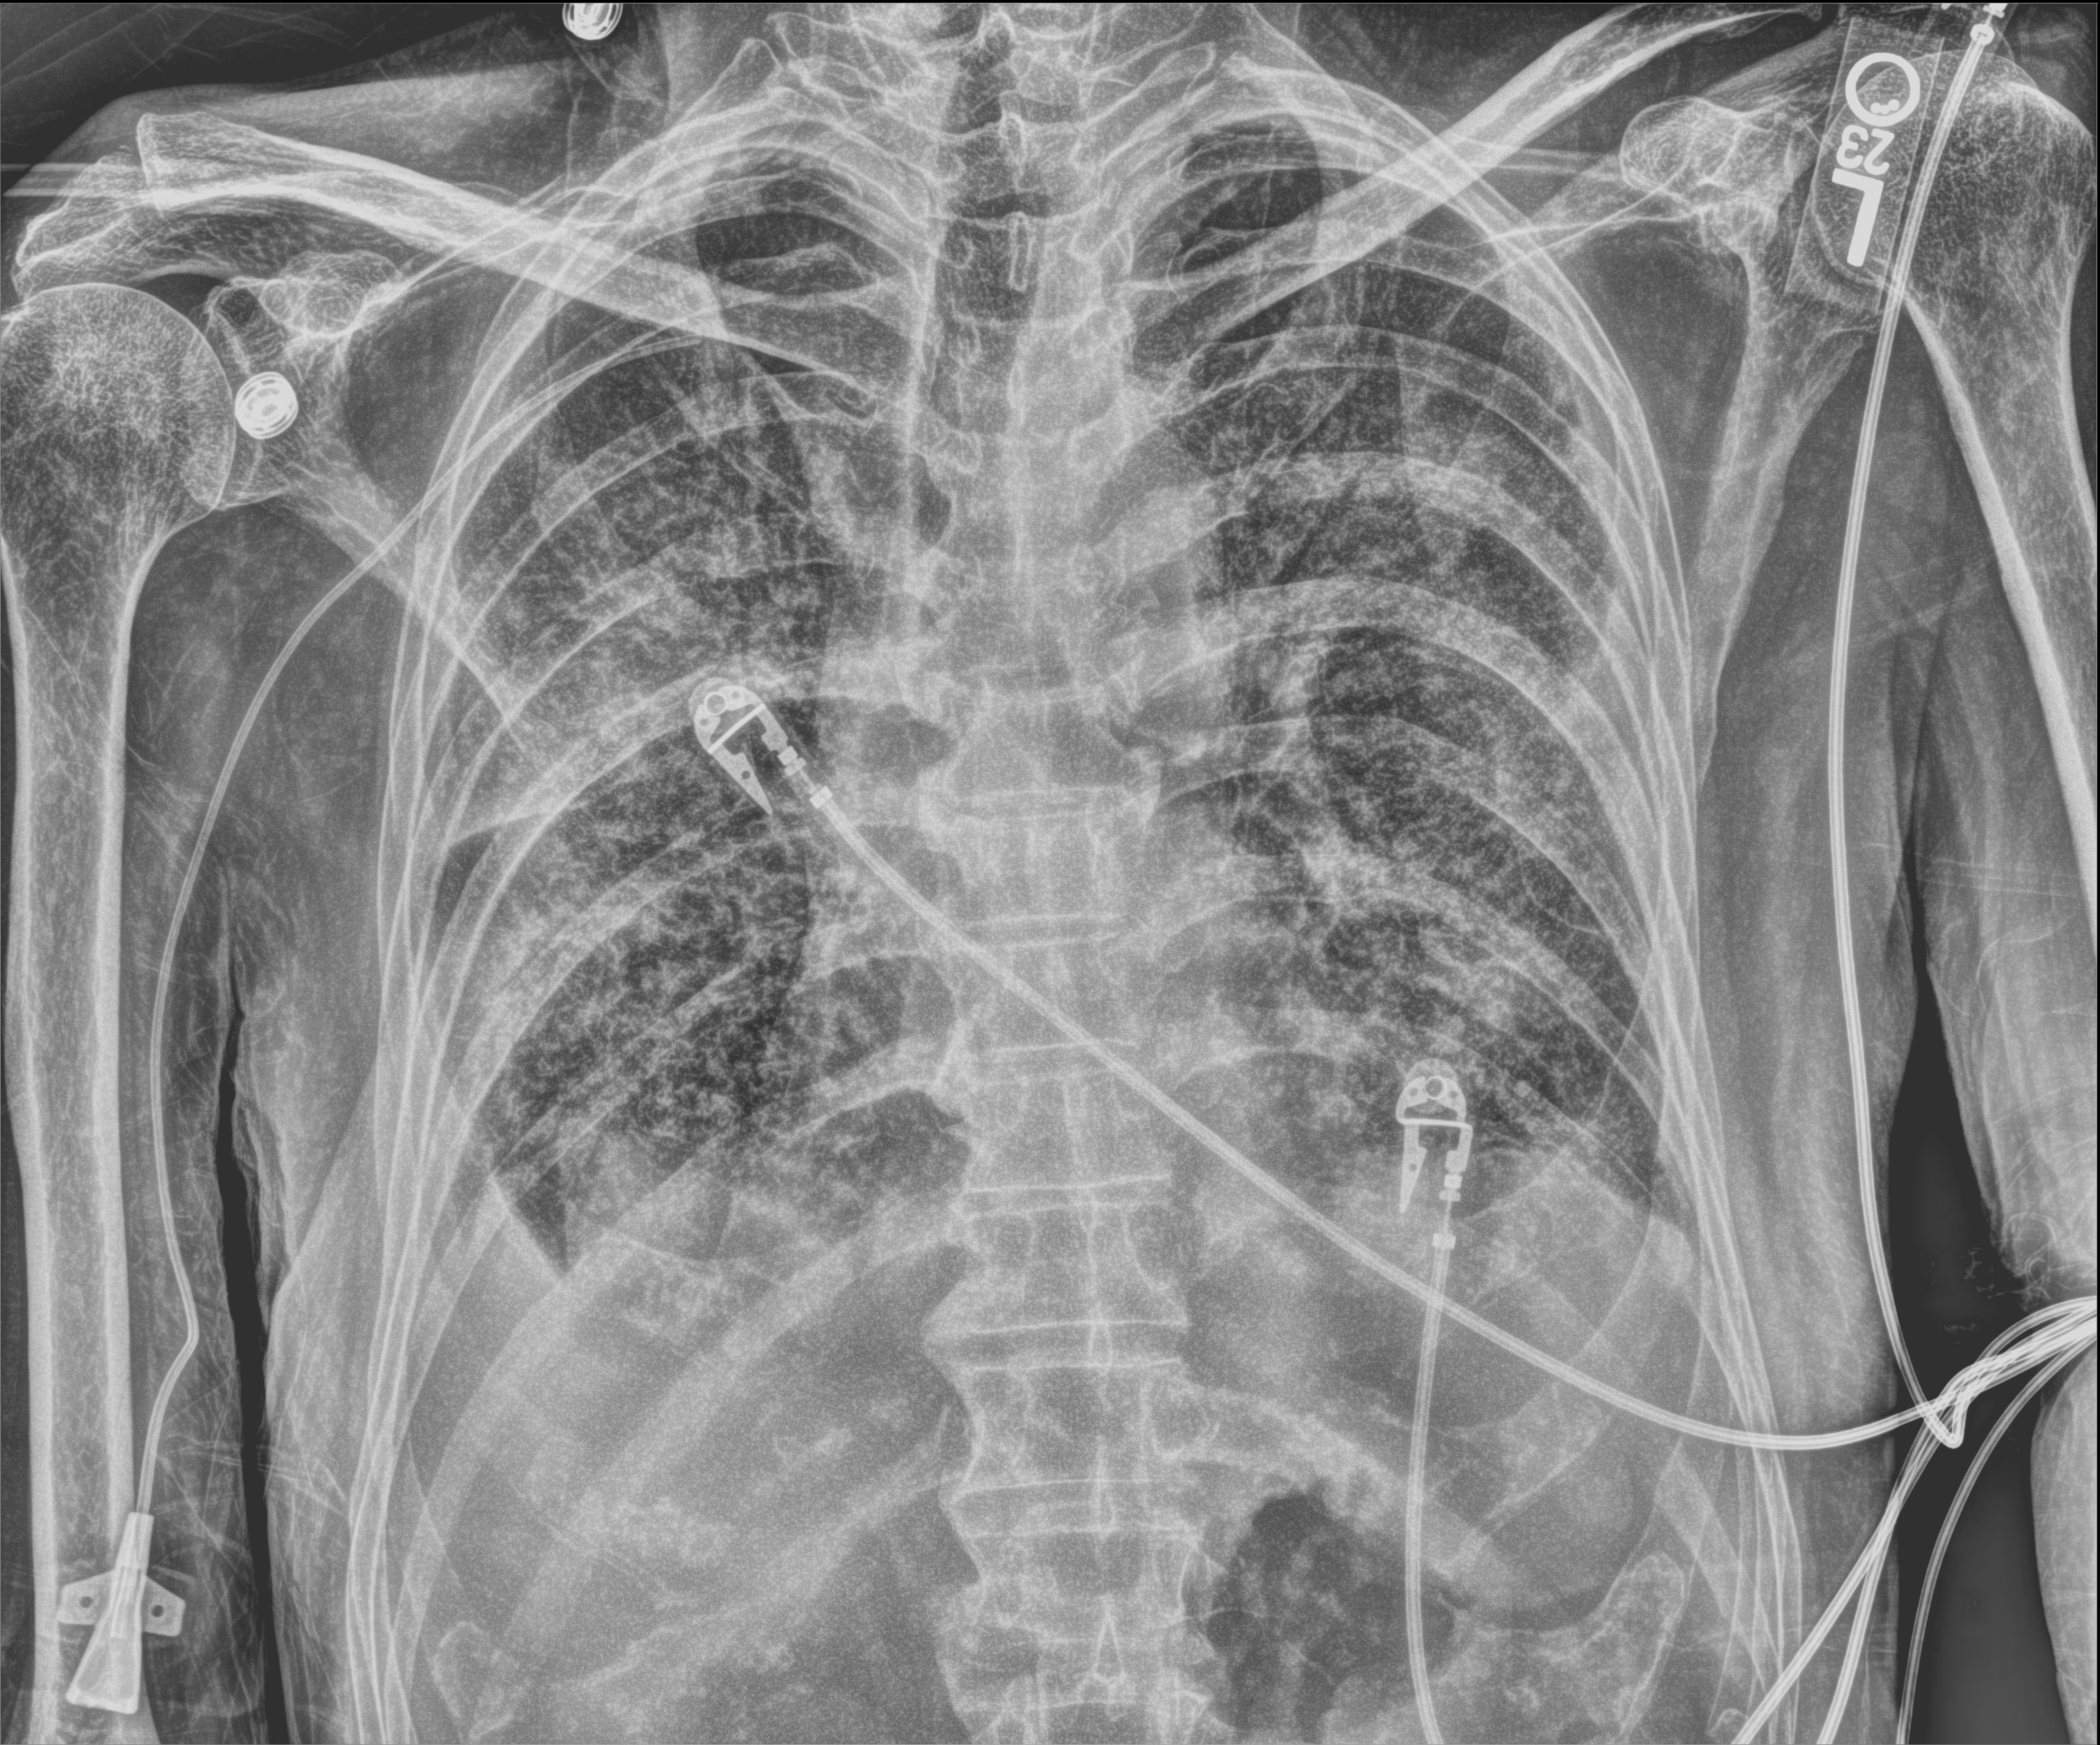
Bedside chest radiograph (computed radiography), anteroposterior (AP) projection. Patient hospitalised with COVID-19; male, aged 60–74 years.
Admission-level facts for this patient (not findings on this image; timing relative to this image not recorded):
- smoking status (admission record): current
- hypertension (admission record): yes